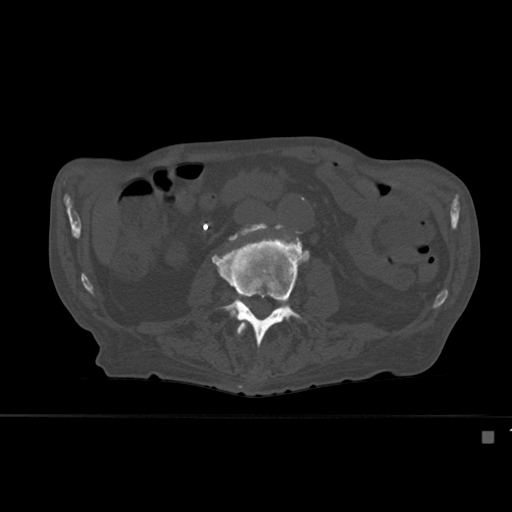
CT including the spine, one axial slice; slice 213 of 527 in the series (ordered by position); bone window (W 1800 / L 400 HU); 512 × 512 image matrix, field of view 373 × 373 mm. Male patient, age 78 years. Case-level facts recorded for this patient, not image findings: primary cancer: prostate.
Annotated regions visible in this slice (semi-automatically segmented with operator editing):
- L2 vertebra: bounding box [x1, y1, x2, y2] px = [236, 320, 258, 370]
- L3 vertebra: [212, 227, 318, 373]
- L4 vertebra: [229, 227, 280, 319]